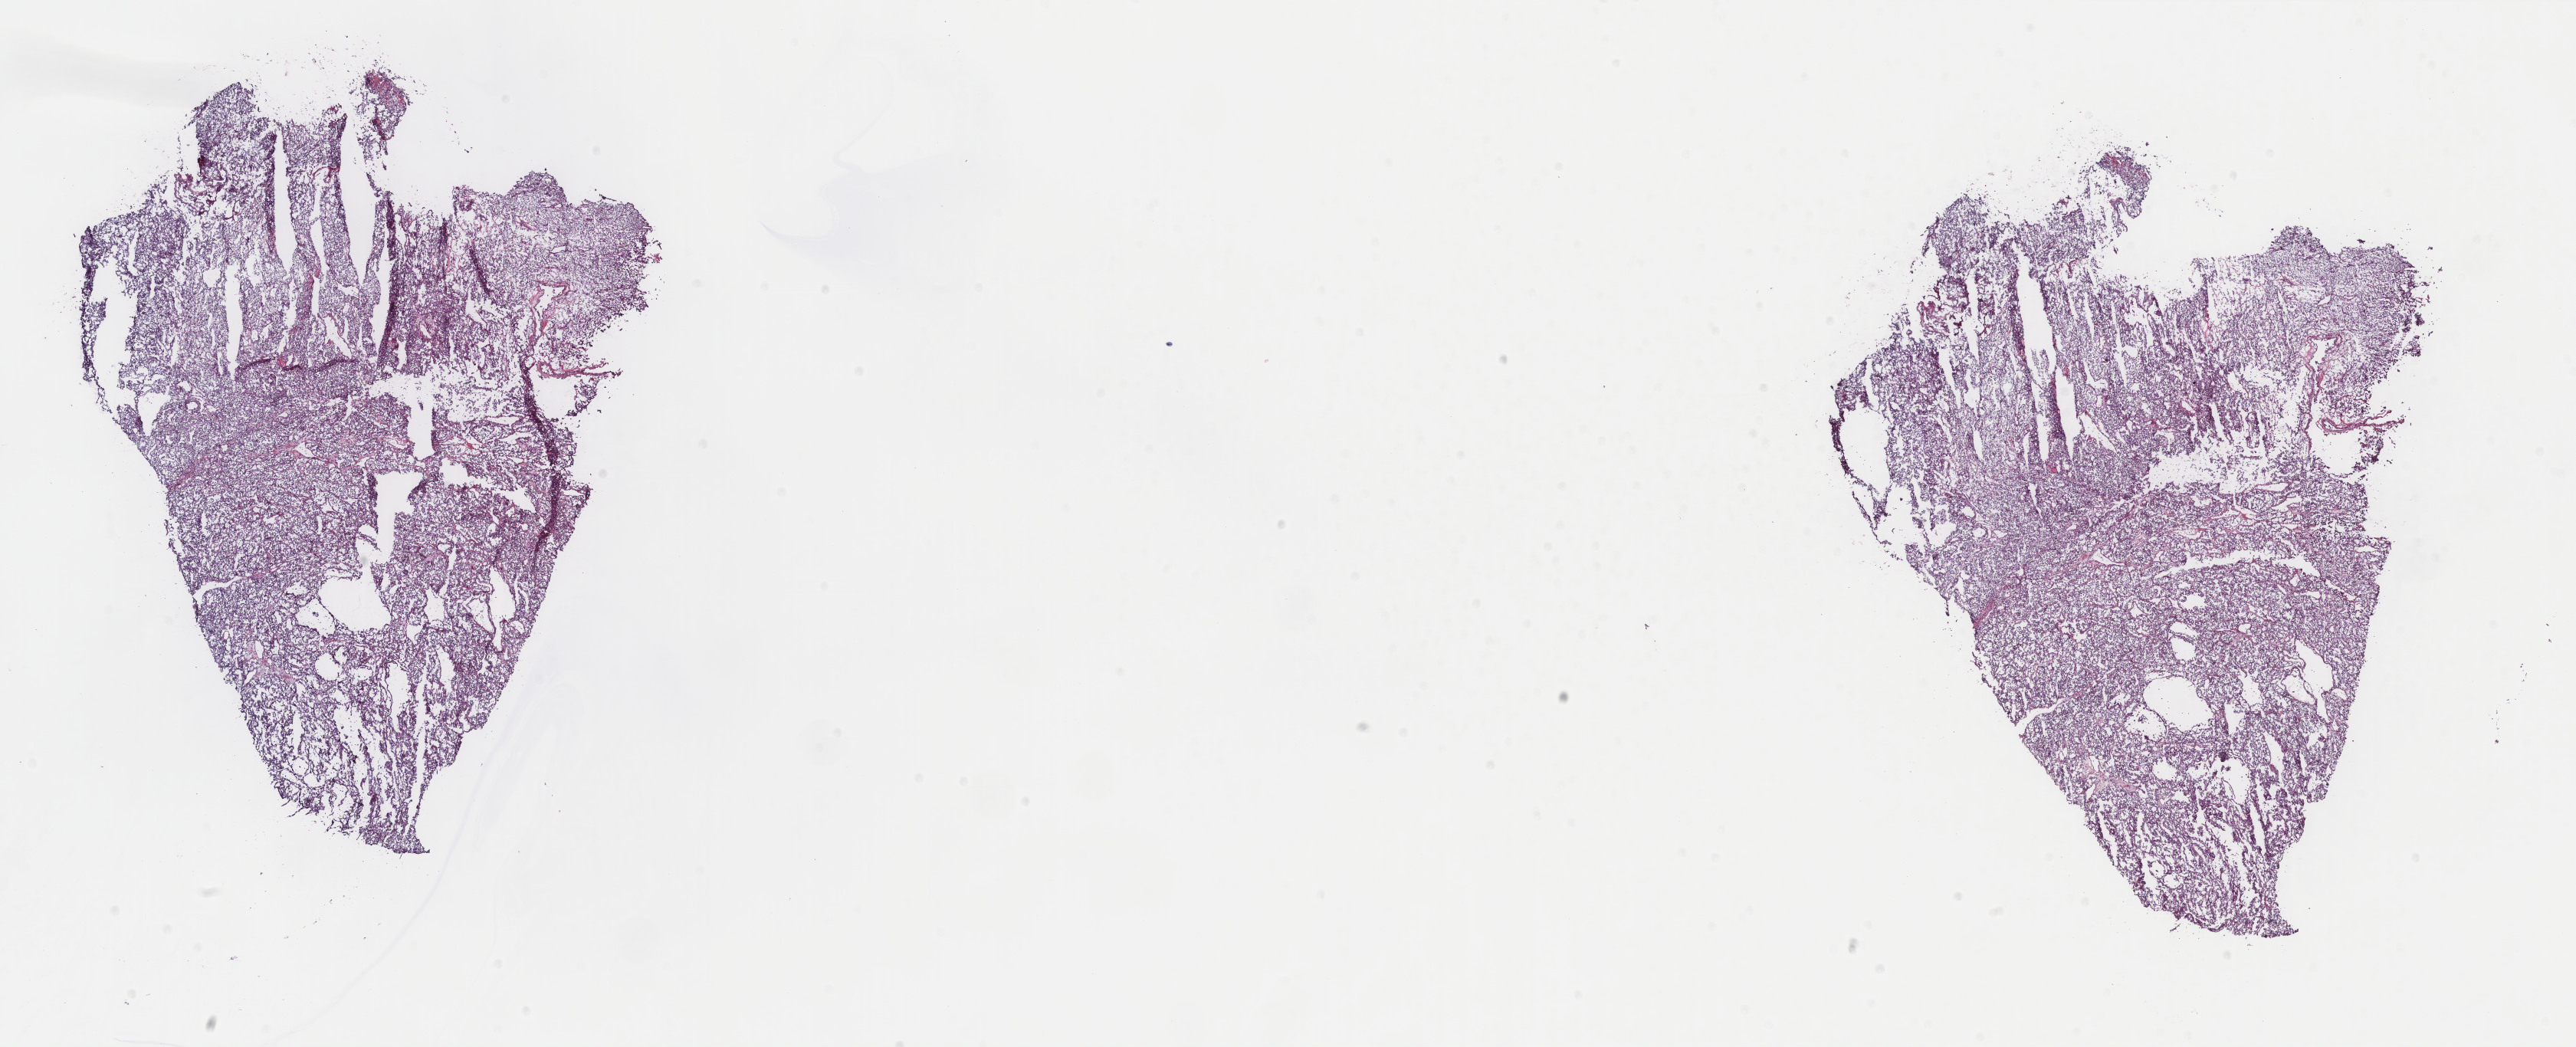
Whole-slide histology image, H&E, a low-resolution overview of the entire scanned area, about 26.7 x 10.8 mm; frozen section from the top of the tissue portion; sample: primary tumour, kidney. Male, age 68 years at initial diagnosis. Composition of this section per pathologist review: tumour cells 90%, tumour nuclei 90%.
Diagnosis: Clear cell adenocarcinoma, NOS.